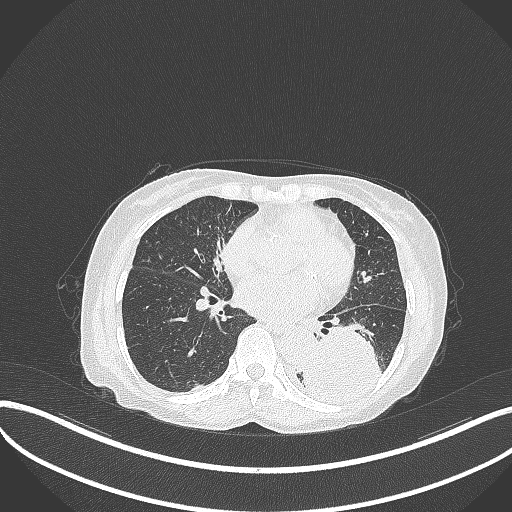
Chest CT, one axial slice. Position 136 of 370 along the scan axis. Lung window (W 1500 / L -600 HU). 1 mm slice thickness. 512 × 512 image matrix, field of view 400 × 400 mm. Female patient, age 78 years. From the clinical record (not read from this slice): clinical TNM (as recorded): T3 N0 M1.
Annotated regions visible in this slice (rectangle marked by the reading radiologist):
- lung tumour (recorded histology: squamous cell carcinoma): bounding box <297,325,383,407> (left, top, right, bottom; pixels)